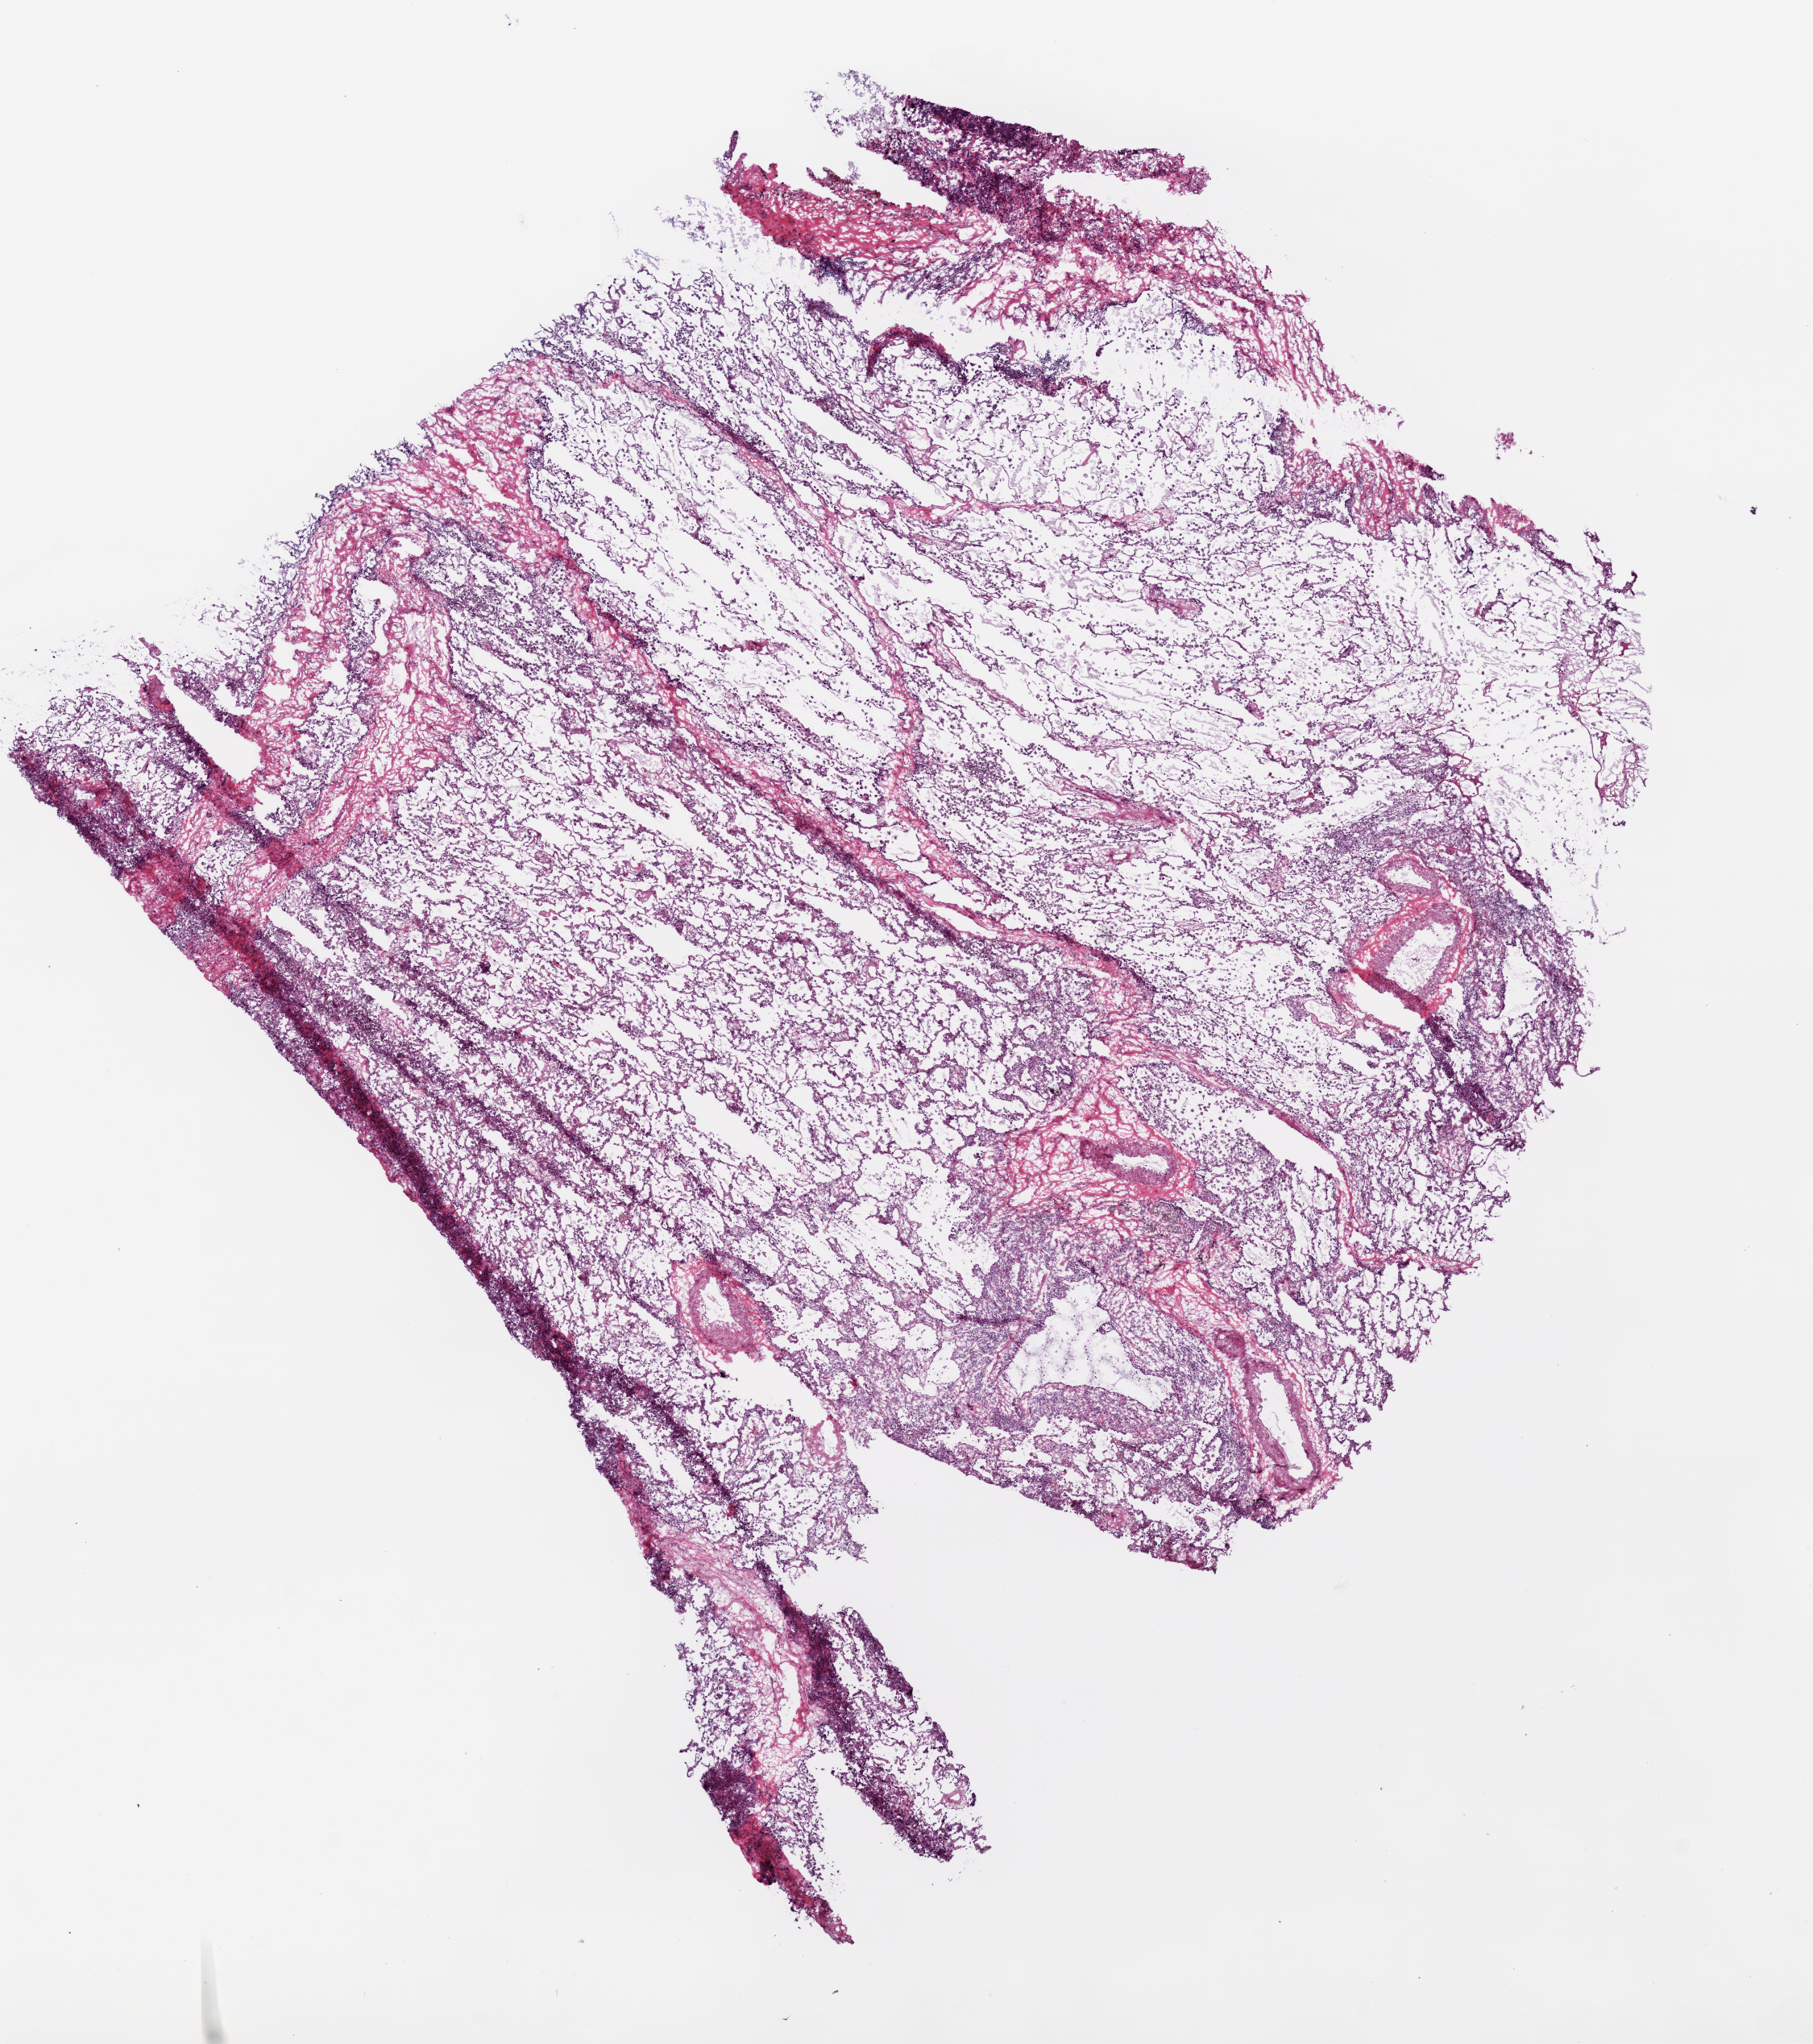
H&E whole-slide image, shown as a low-resolution overview of the whole scanned area (about 9.0 x 10.2 mm). Frozen section from the top of the tissue portion. Sample: solid tissue normal (non-tumour tissue), lung. Patient: male, age at initial diagnosis 55 years.
This section: solid tissue normal (non-tumour) sample from the same patient. Patient diagnosis: Squamous cell carcinoma, NOS.